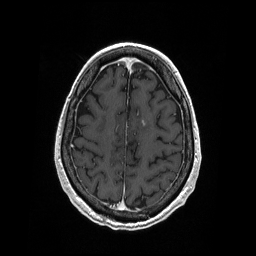
Brain MRI from a brain-tumour surgery series, one axial slice; position 64 of 208 along the scan axis; T1-weighted post-contrast; 1 mm slice thickness; 256 × 256 image matrix, field of view 256 × 256 mm. From the clinical record (not read from this slice): histopathology: Primary diffuse large B-cell lymphoma.
Annotated regions visible in this slice (manually delineated by an expert):
- tumour: bounding box (x1, y1, x2, y2) in pixels: (142, 120, 146, 127)